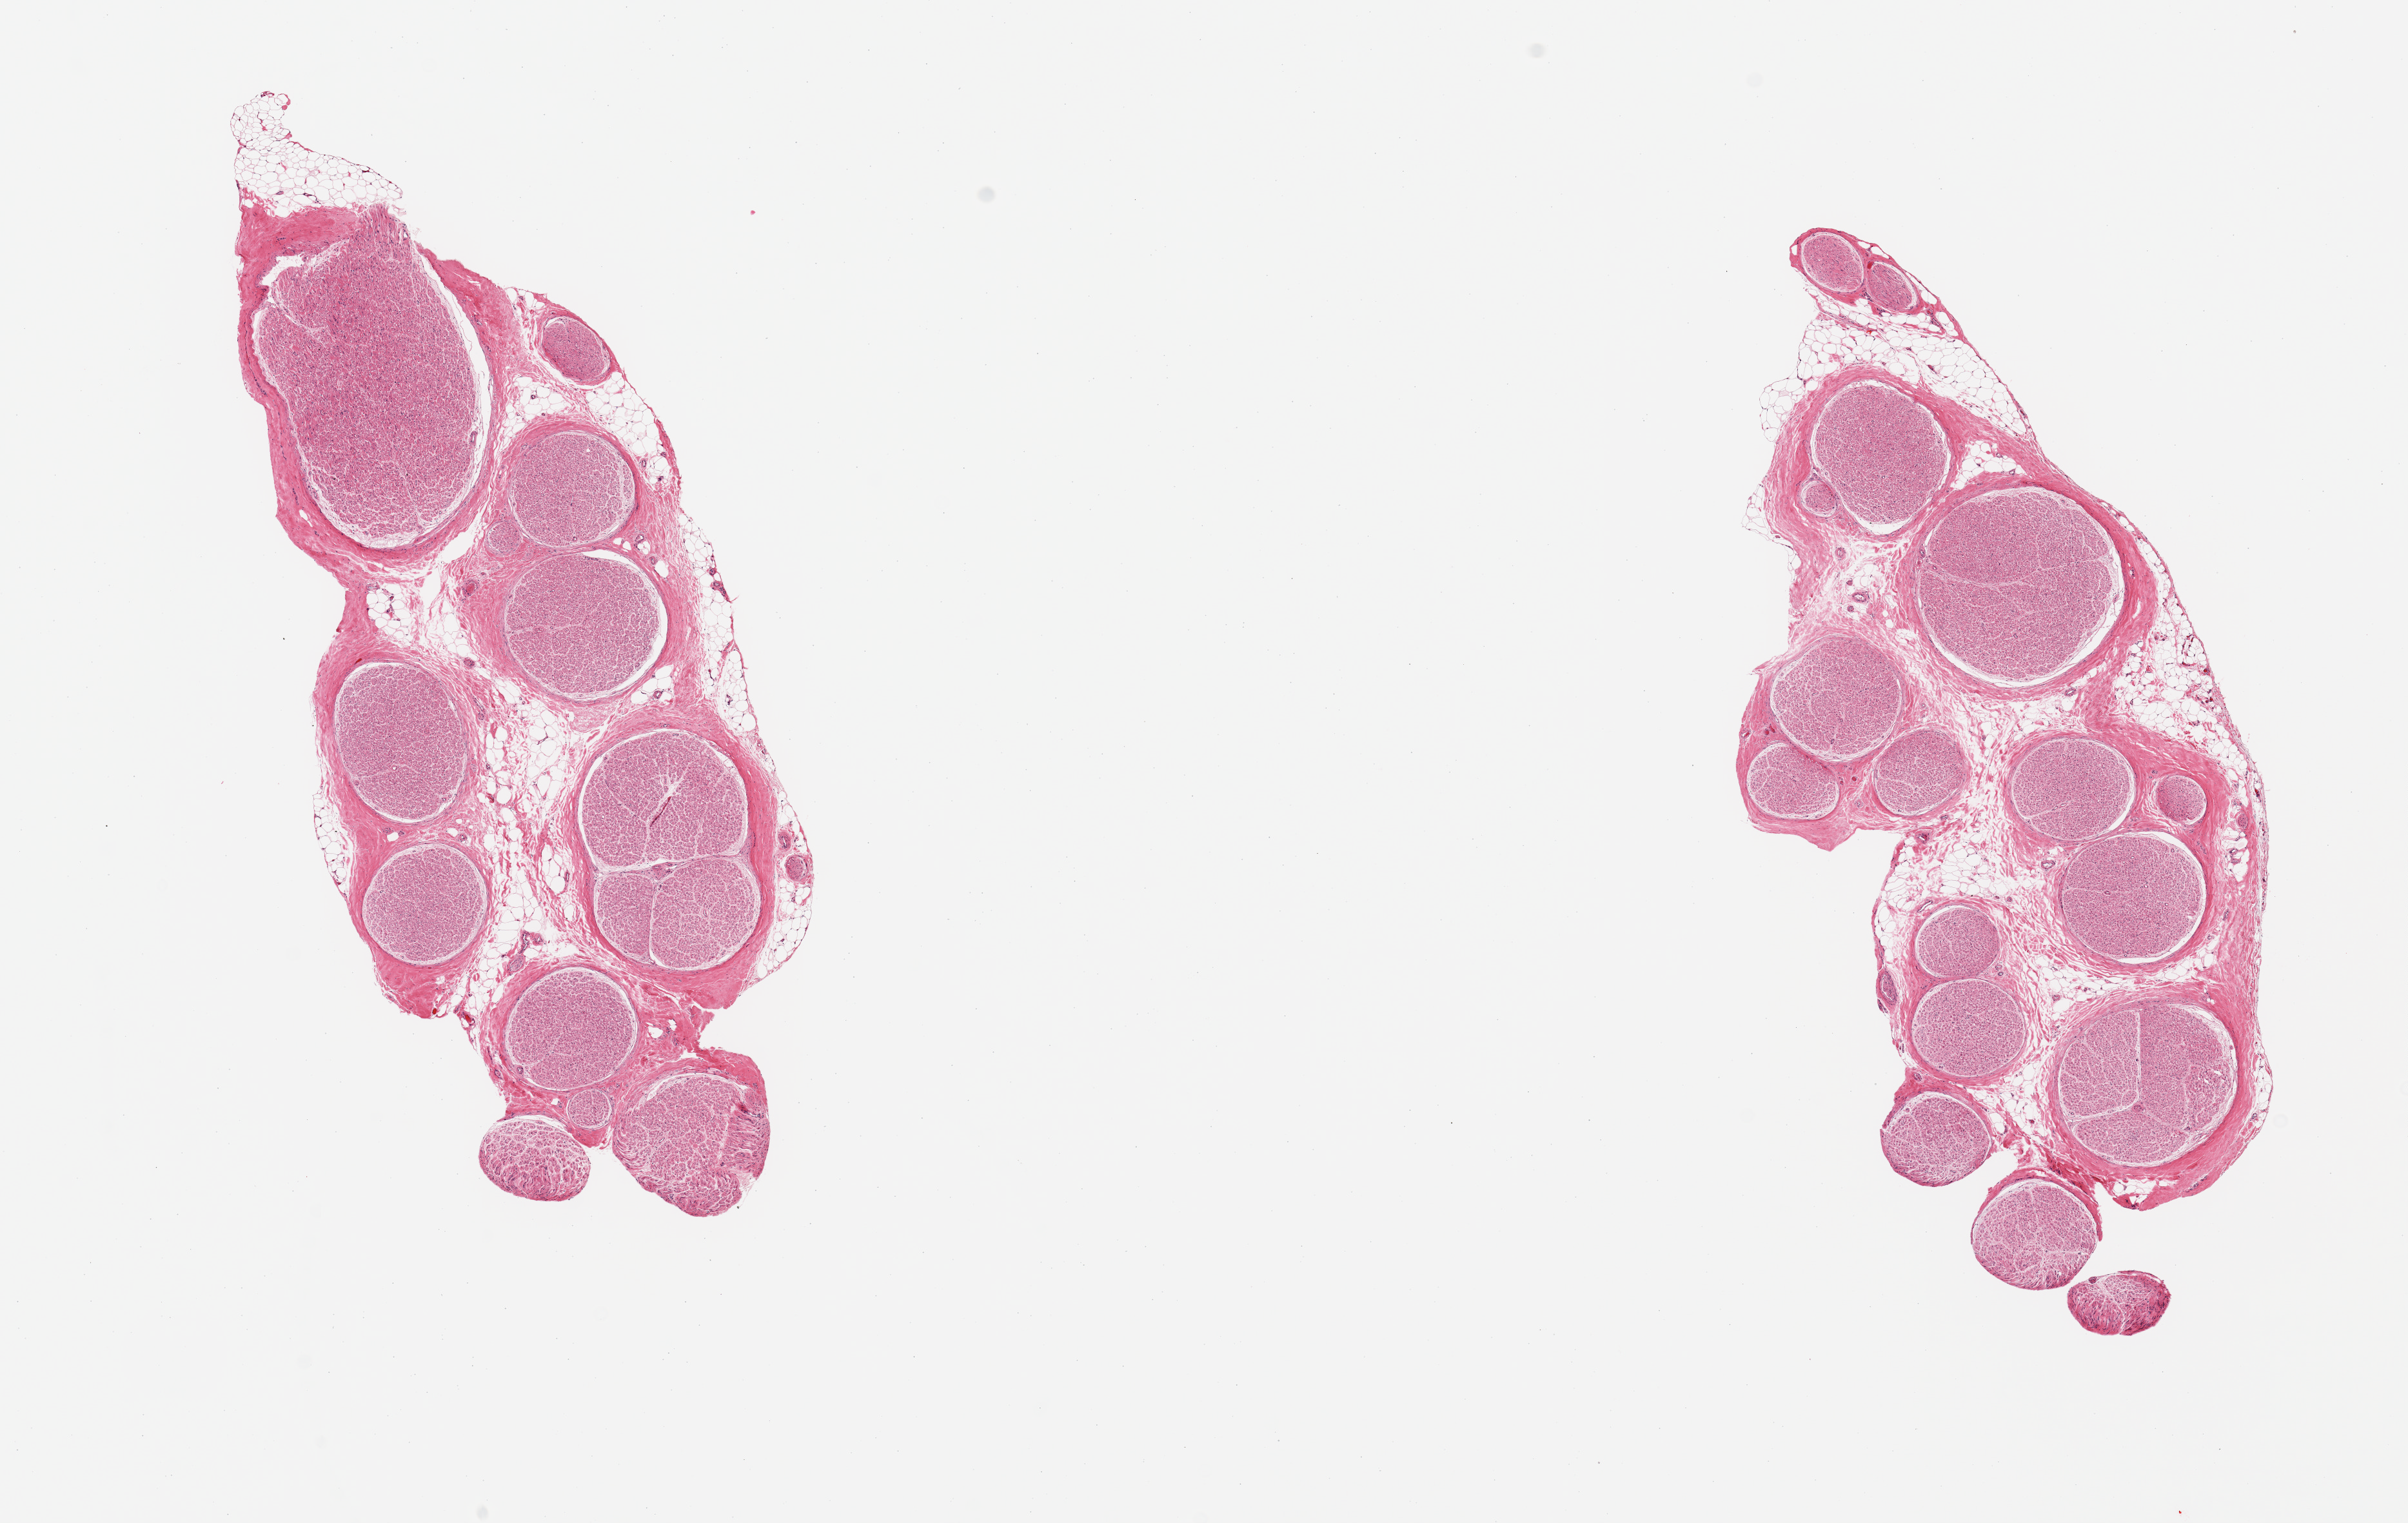
Whole-slide image, haematoxylin and eosin stain — whole scanned area (about 14.8 x 9.3 mm, acquisition: 20x scan) shown as a low-resolution overview; PAXgene-fixed paraffin-embedded (PFPE) section; sampled site (target tissue): tibial nerve; donor tissue sample. Donor sex: male.
Pathologist's review note for this sample: 2 pieces;~15% internal/external fat.